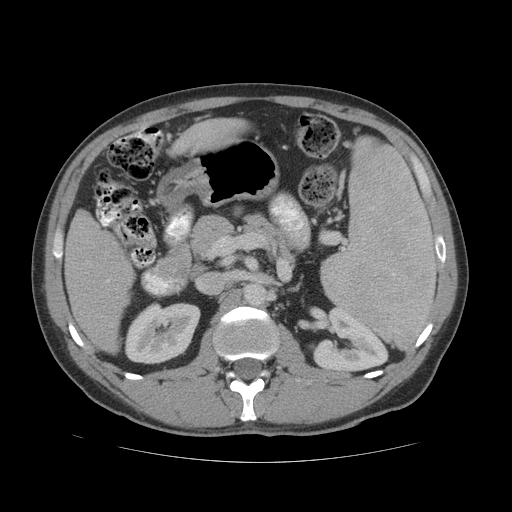
Contrast-enhanced abdominal CT (liver protocol), one axial slice; slice 22 of 81 in the series (ordered by position); soft-tissue window (W 400 / L 40 HU); 2.5 mm slice thickness; 512 × 512 image matrix, field of view 400 × 400 mm. Case-level facts recorded for this patient, not image findings: diagnosis: hepatocellular carcinoma (patient treated with transarterial chemoembolisation; whether this scan precedes or follows treatment is not stated here); TNM stage (as recorded): Stage-IVB; Child-Pugh class: B; tumour differentiation: well differentiated; tumour nodularity: multinodular.
Structures marked on this image (semi-automatically segmented with operator editing):
- liver parenchyma outside the tumour (the mass and vessels are separate outlines, so this box may not span the whole liver): box from (x=64, y=120) to (x=238, y=352) px
- liver vessels: (x=107, y=280)–(x=109, y=282)